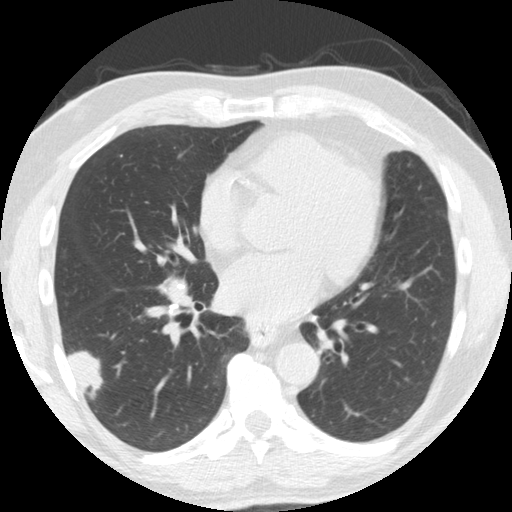
Chest CT (low-dose screening protocol), one axial image, second annual screen, lung window (W 1500 / L -600 HU), slice 97 of 174 in the series, 512 × 512 image matrix, field of view 341 × 341 mm. Male participant, aged 61 years at enrolment. Former smoker at enrolment.
• Expert-annotated lung lesion, box from (x=49, y=325) to (x=117, y=401) px.
• Reader record for this screening exam (exam-level; its link to the box is not recorded): non-calcified nodule or mass ≥4 mm, right lower lobe, 33 × 19 mm, smooth margins, soft tissue attenuation, pre-existing on the prior screen: yes; interval growth: yes.
• Participant outcome: lung cancer diagnosed 30 days after this screen — adenosquamous carcinoma, right lower lobe, poorly differentiated (G3), stage IV (AJCC 6th edition), 45 mm at pathology.